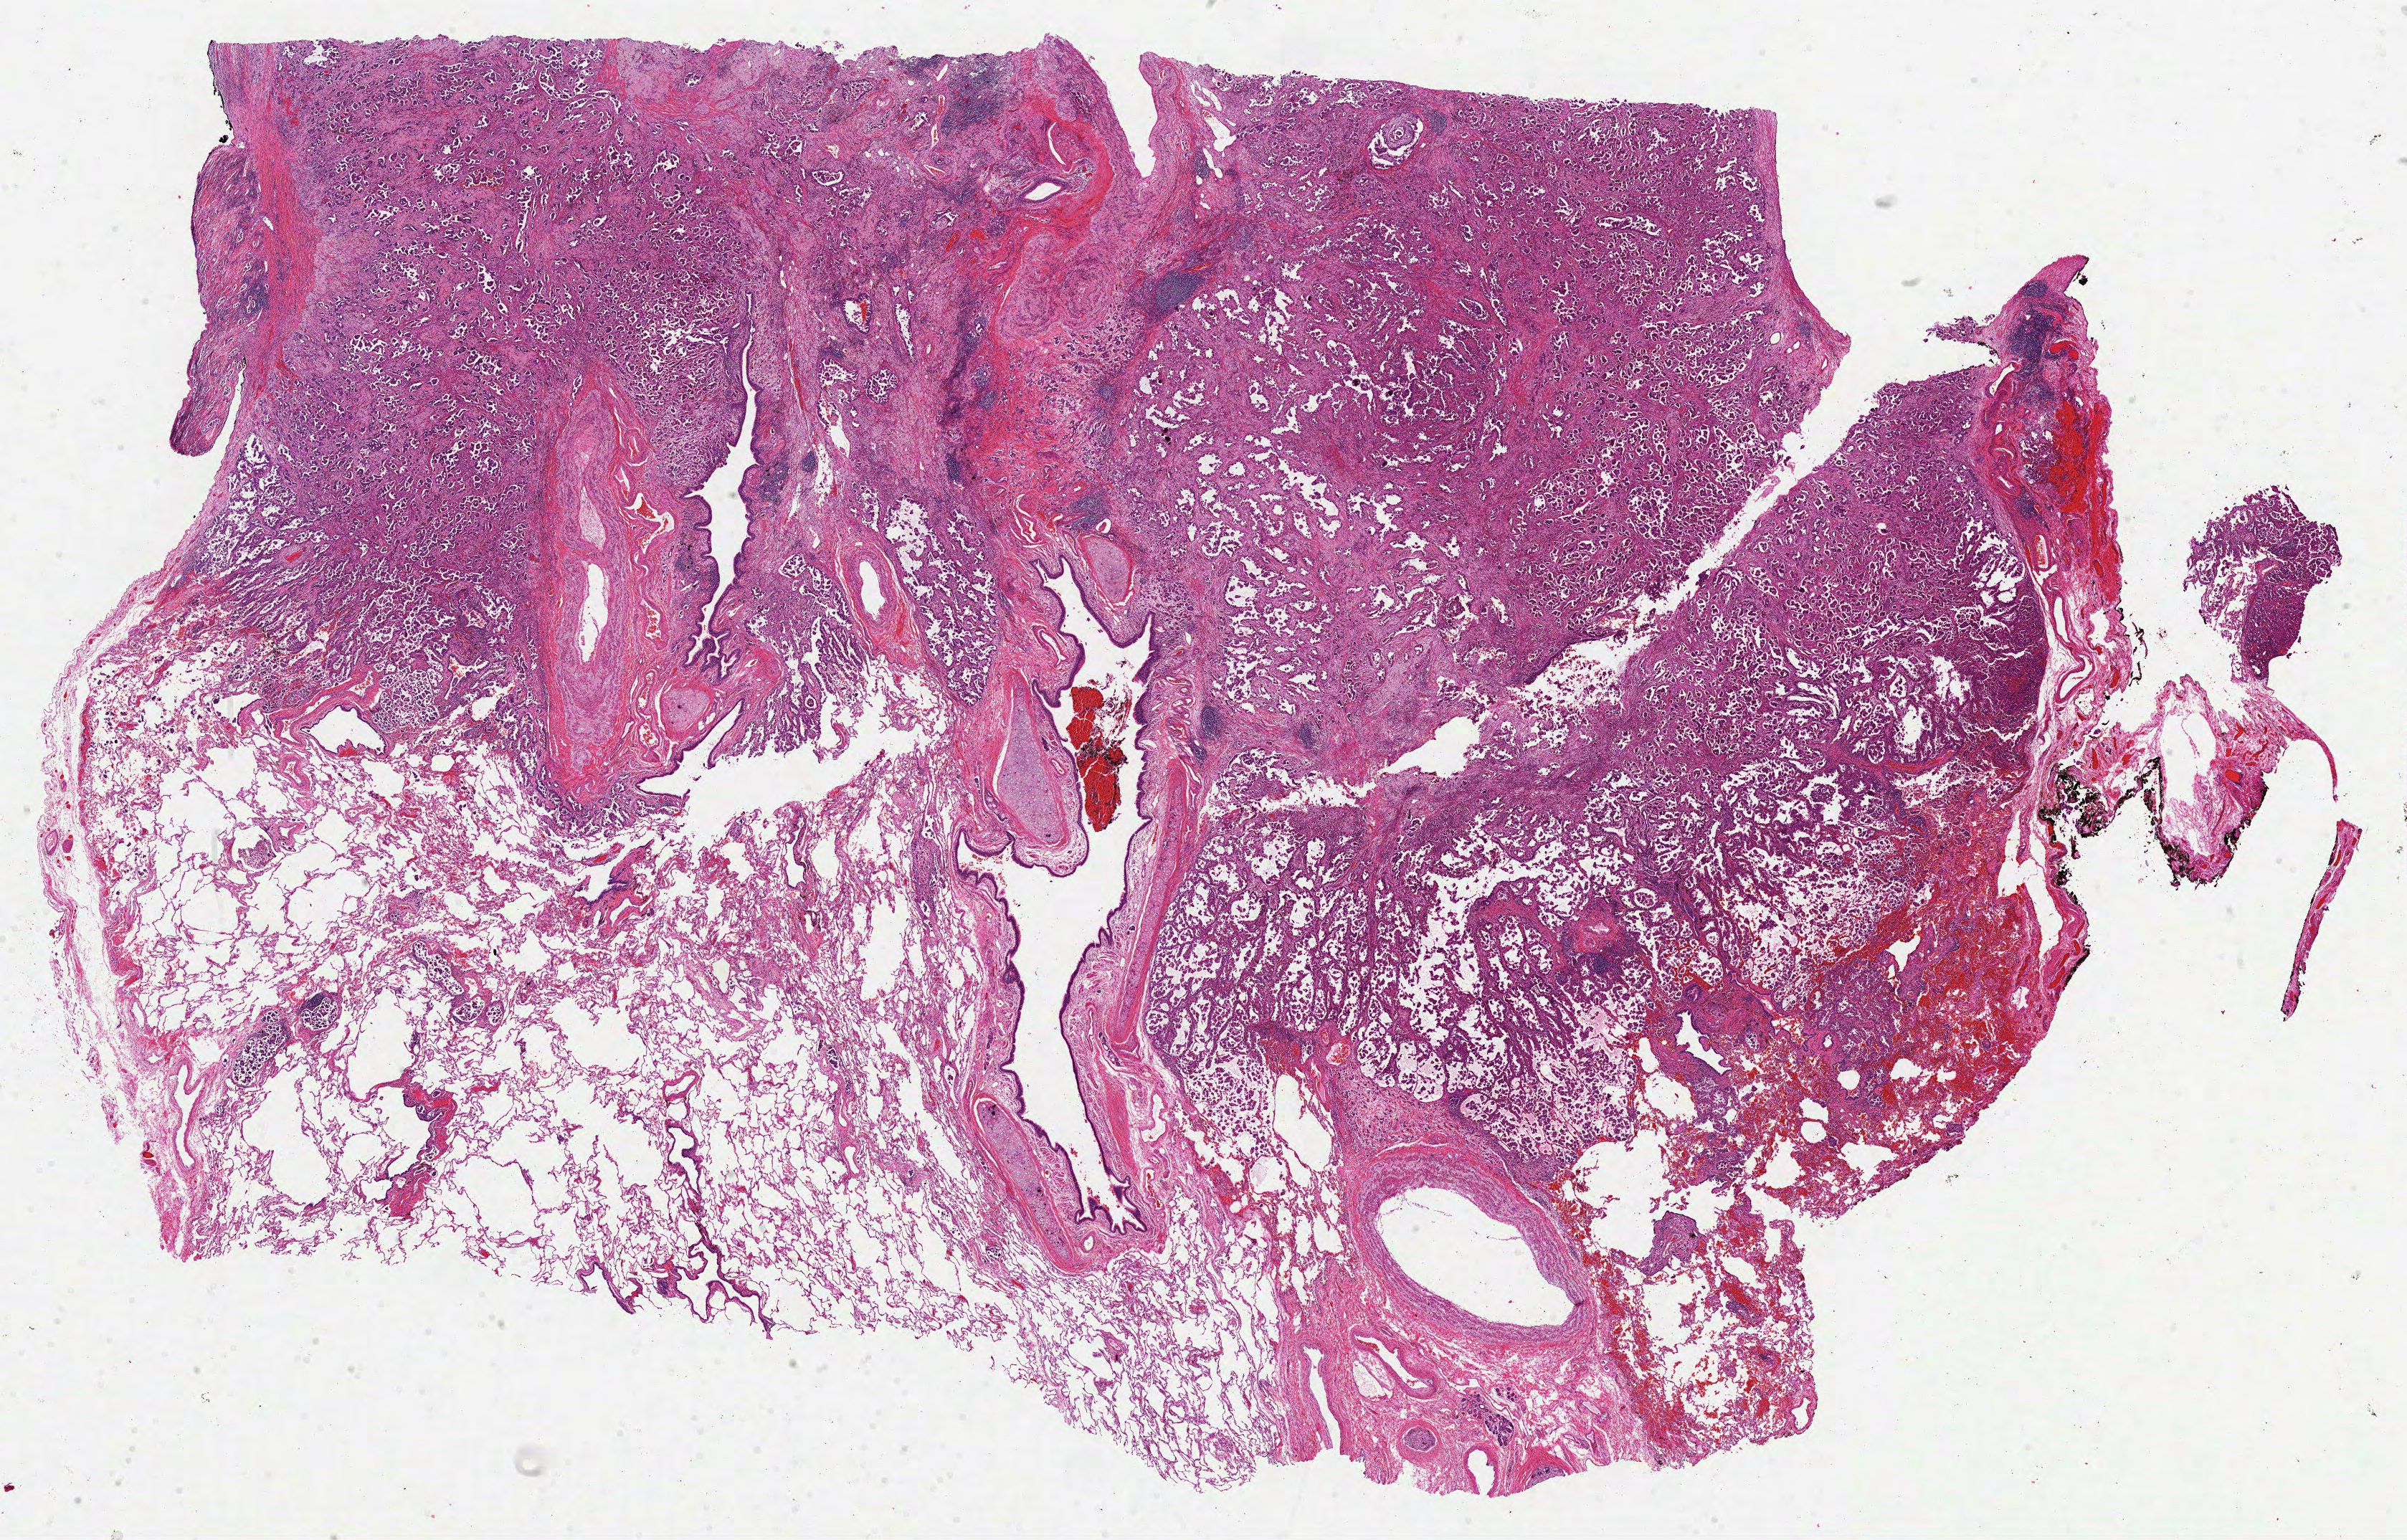
Whole-slide histology image, H&E — shown as a low-resolution overview of the whole scanned area (about 27.1 x 17.3 mm); FFPE section; sample: primary tumour, lung. Female, age 69 years at initial diagnosis.
Pathologic diagnosis: Adenocarcinoma, NOS.